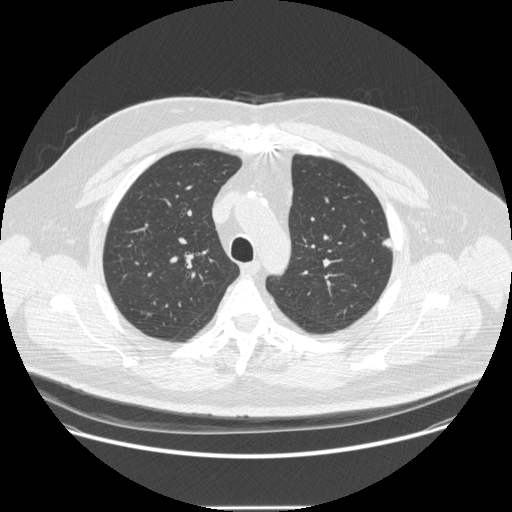
Low-dose screening chest CT, axial slice, second annual screen, lung window (W 1500 / L -600 HU), 1.25 mm slice thickness, standard (soft-tissue) reconstruction kernel (STANDARD), 120 kVp. Male, age 55 years at enrolment. Former smoker at enrolment.
Lesion marked by an expert reader, bounding box (x1, y1, x2, y2) in pixels: (373, 231, 405, 251). The screening reader recorded 2 non-calcified nodules or masses ≥4 mm on this exam (left upper lobe, left upper lobe); which of them this box marks is not recorded. Later outcome: lung cancer diagnosed 60 days after this screen — adenocarcinoma, NOS, left upper lobe, moderately differentiated (G2), stage IA (AJCC 6th edition), 9 mm at pathology.